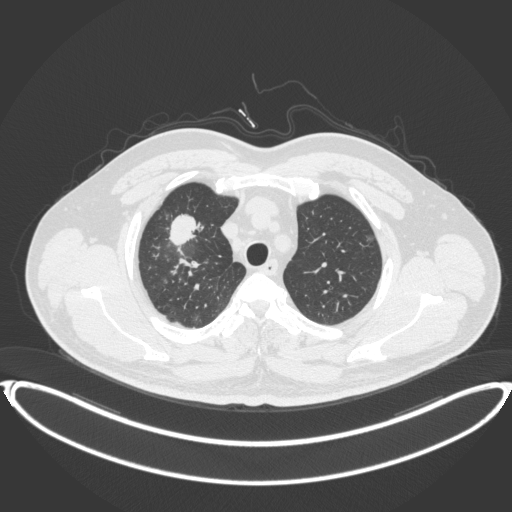
Chest CT, one axial slice. Slice 313 of 399 in the series (ordered by position). Reconstruction kernel B31f. Lung window (W 1500 / L -600 HU). 1 mm slice thickness. 512 × 512 image matrix, field of view 445 × 445 mm. Patient: male, 53 years. Case-level facts recorded for this patient, not image findings: clinical TNM (as recorded): T2a N0 M0.
Annotated regions visible in this slice (rectangle marked by the reading radiologist):
- lung tumour (recorded histology: adenocarcinoma): bounding box (x1, y1, x2, y2) in pixels: (165, 207, 201, 250)